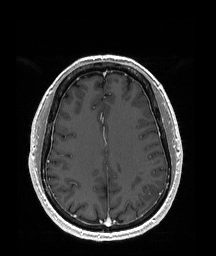
Brain MRI from a brain-tumour surgery series, one axial slice; slice 73 of 192 in the series (ordered by position); T1-weighted post-contrast; 1 mm slice thickness; 216 × 256 image matrix. From the clinical record (not read from this slice): histopathology: Glioblastoma; WHO grade: 4; IDH mutation: no; tumour location: Left Temporal Parietal.
Outlined on this slice (expert manual segmentation):
- tumour: bounding box <142,184,160,206> (left, top, right, bottom; pixels)